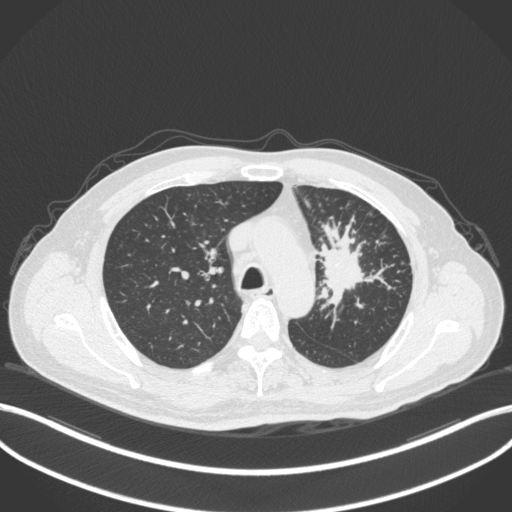
Chest CT, one axial slice; position 253 of 386 along the scan axis; reconstruction kernel B31f; lung window (W 1500 / L -600 HU); 512 × 512 image matrix, field of view 400 × 400 mm. Male patient, age 69 years. From the clinical record (not read from this slice): clinical TNM (as recorded): T2a N2 M0; histopathological grade: G2-3.
Outlined on this slice (rectangle marked by the reading radiologist):
- lung tumour (recorded histology: adenocarcinoma): bounding box [x1, y1, x2, y2] px = [315, 219, 379, 309]